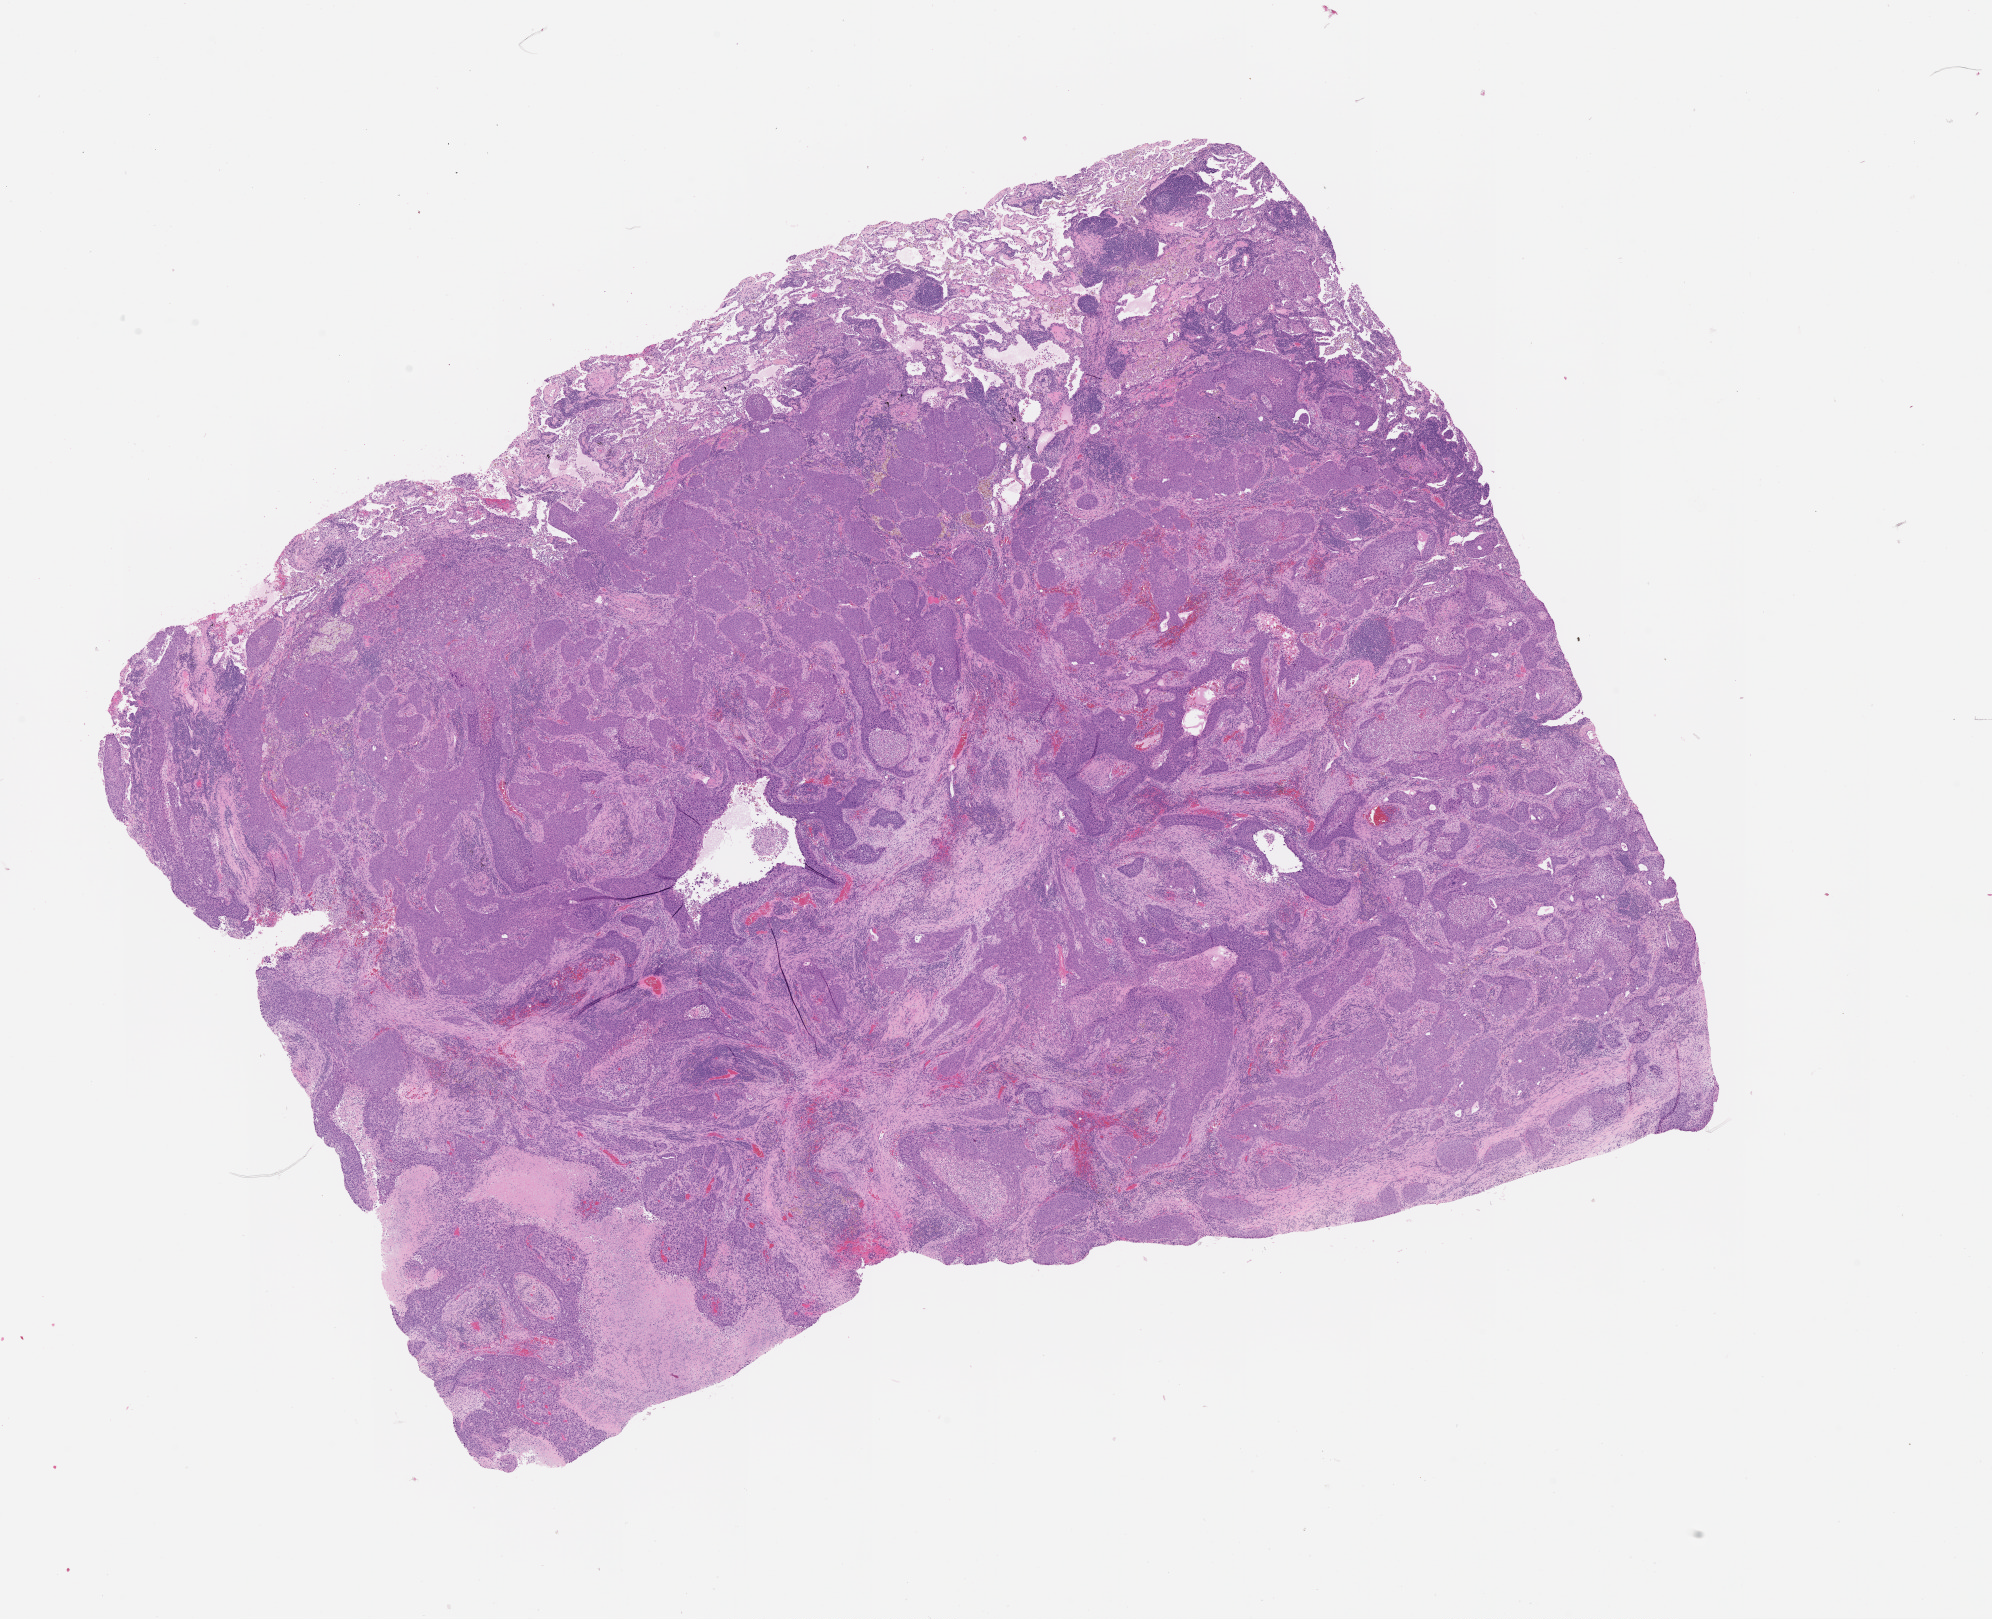
Hematoxylin and eosin (H&E) stained whole-slide image, low-resolution overview of the scanned area, about 16.0 x 13.0 mm; lung, tumour tissue. 54-year-old female patient.
* patient diagnosis (cohort enrolment): squamous cell carcinoma (lung)